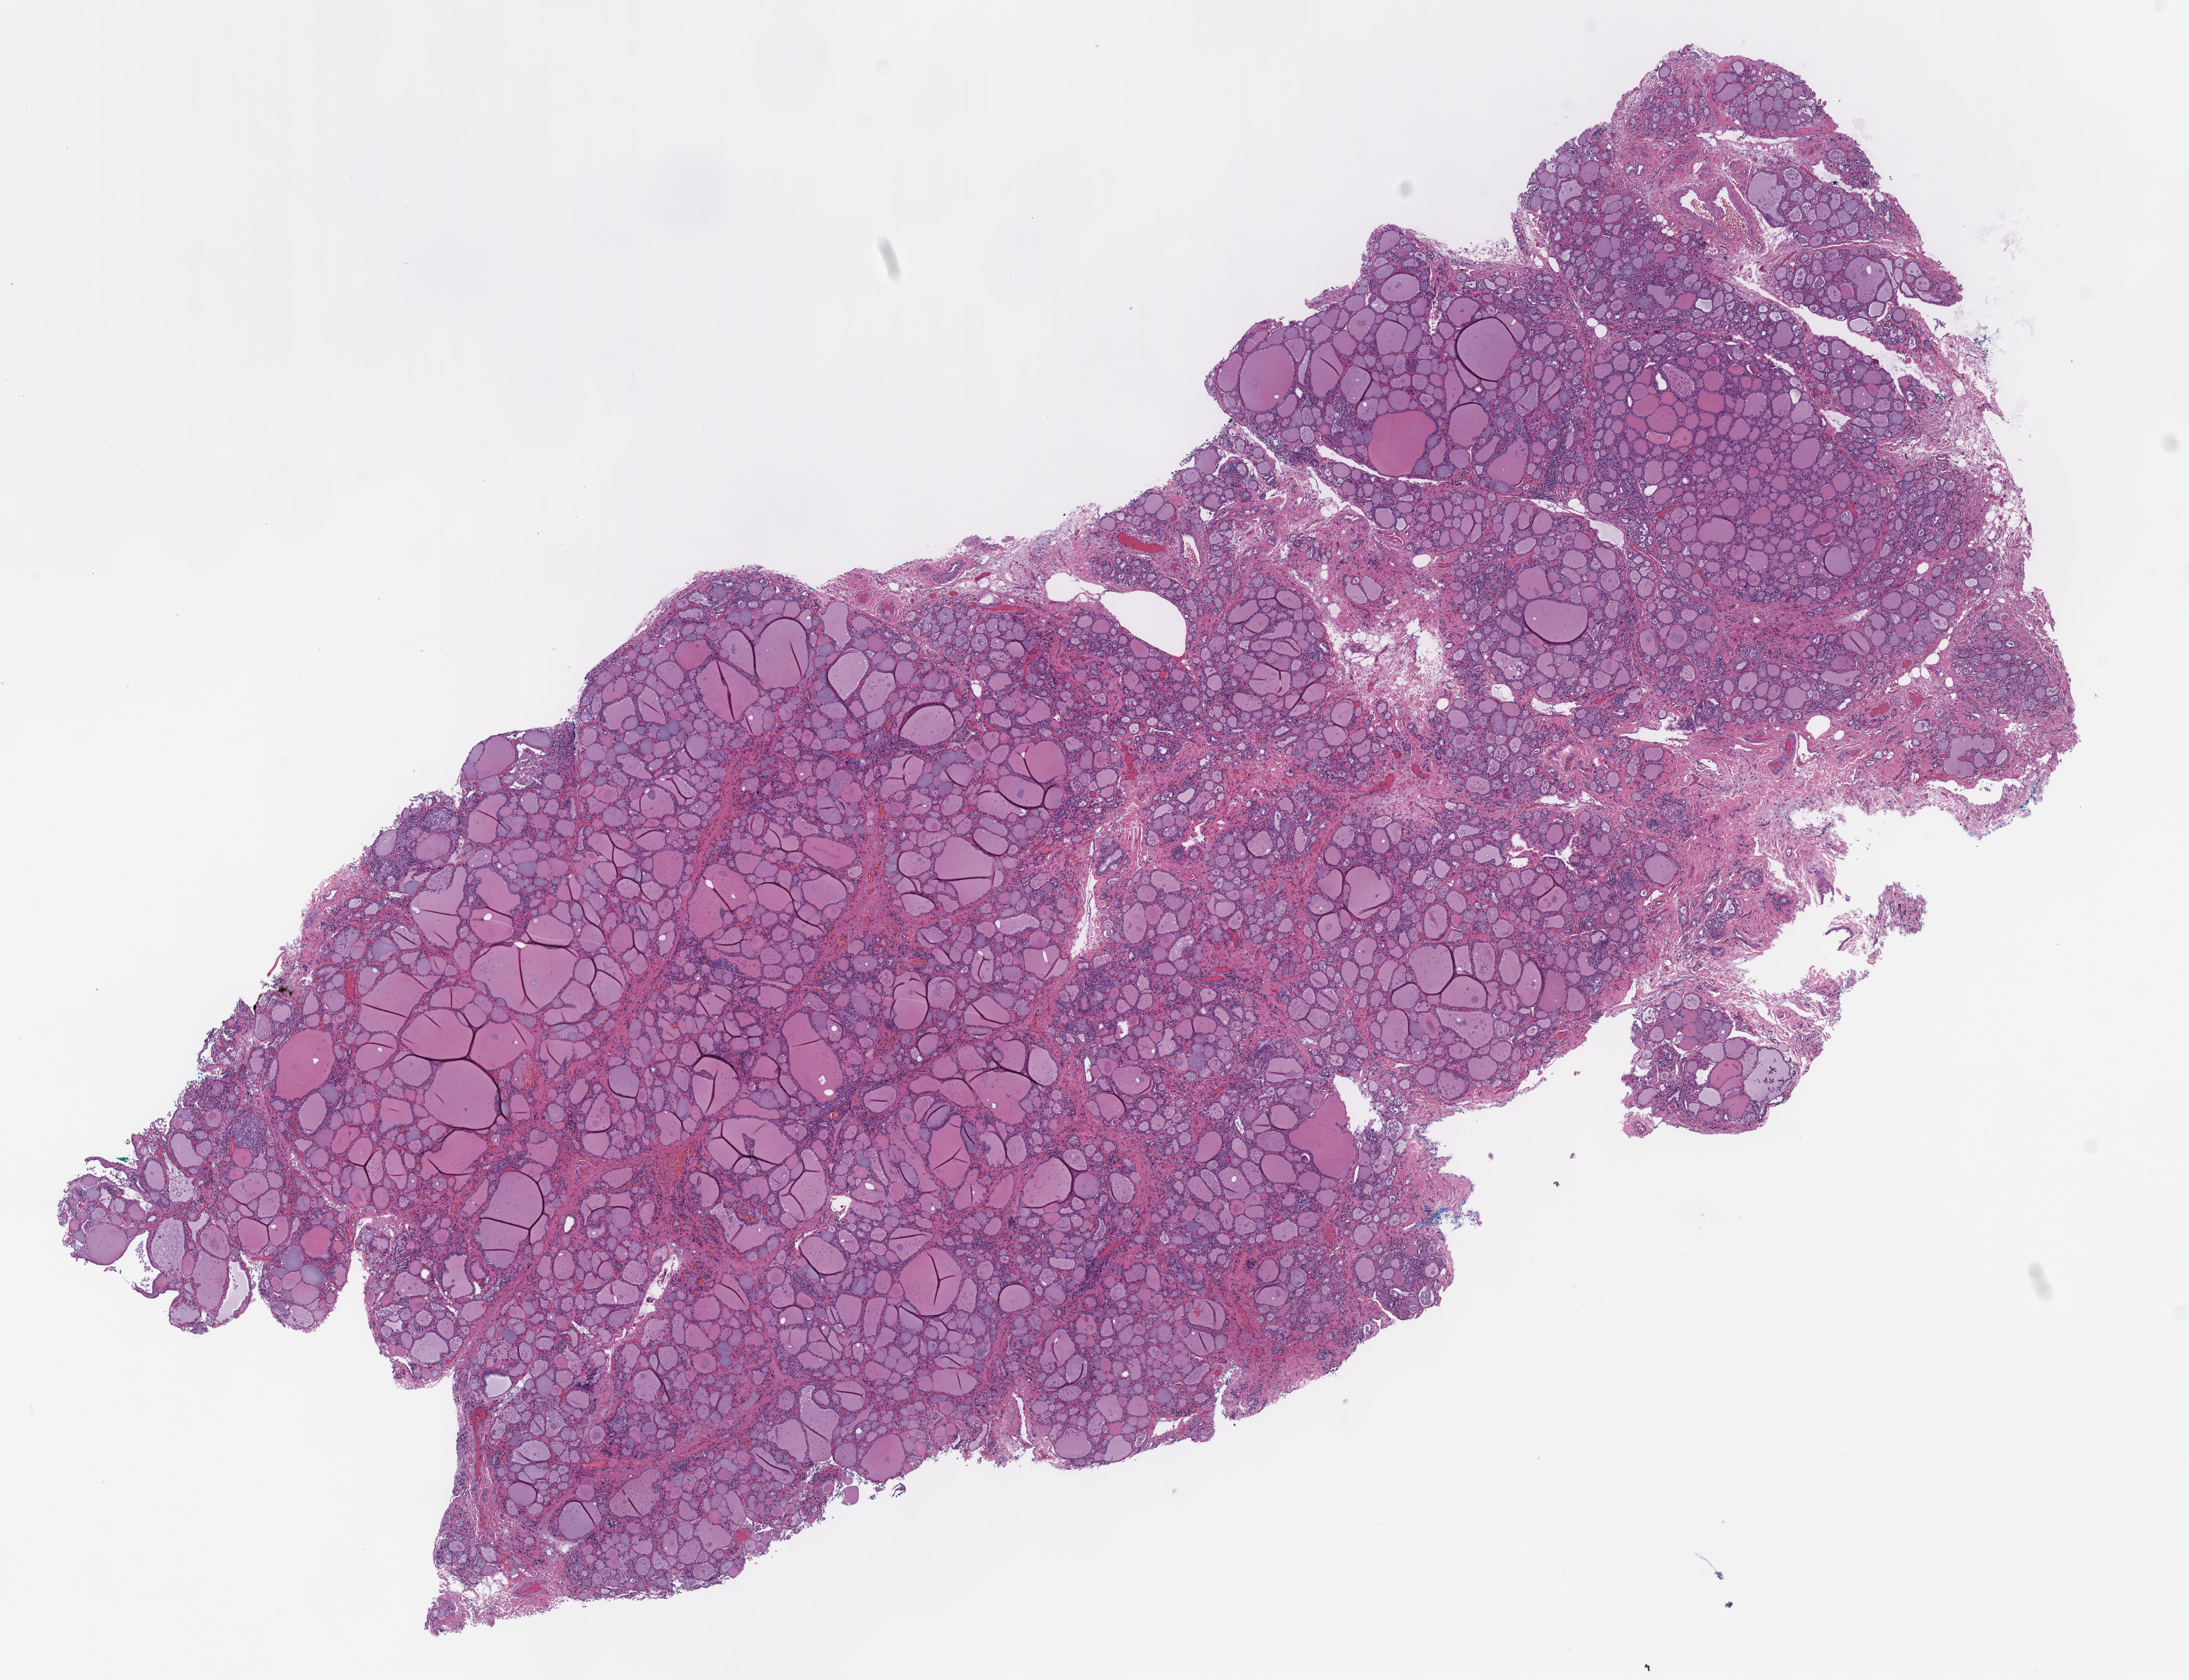
Whole-slide histology image, H&E-stained, shown as a low-resolution overview of the whole scanned area (about 12.2 x 9.4 mm, acquisition: 40x scan), formalin-fixed paraffin-embedded (FFPE) diagnostic section, sample: primary tumour, thyroid. Female patient; age at initial diagnosis 64 years.
Pathologic diagnosis: Papillary adenocarcinoma, NOS (thyroid gland).